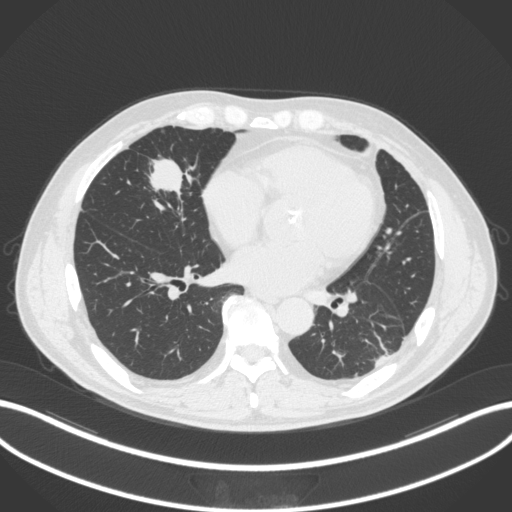
Chest CT, one axial slice. Slice 114 of 399 in the series (ordered by position). 120 kVp. Lung window (W 1500 / L -600 HU). 1 mm slice thickness. 512 × 512 image matrix, field of view 400 × 400 mm. Male patient, age 59 years. From the clinical record (not read from this slice): clinical TNM (as recorded): T2a N1 M0.
Outlined on this slice (bounding box drawn by a radiologist):
- lung tumour (recorded histology: adenocarcinoma): bounding box [x1, y1, x2, y2] px = [139, 152, 198, 205]